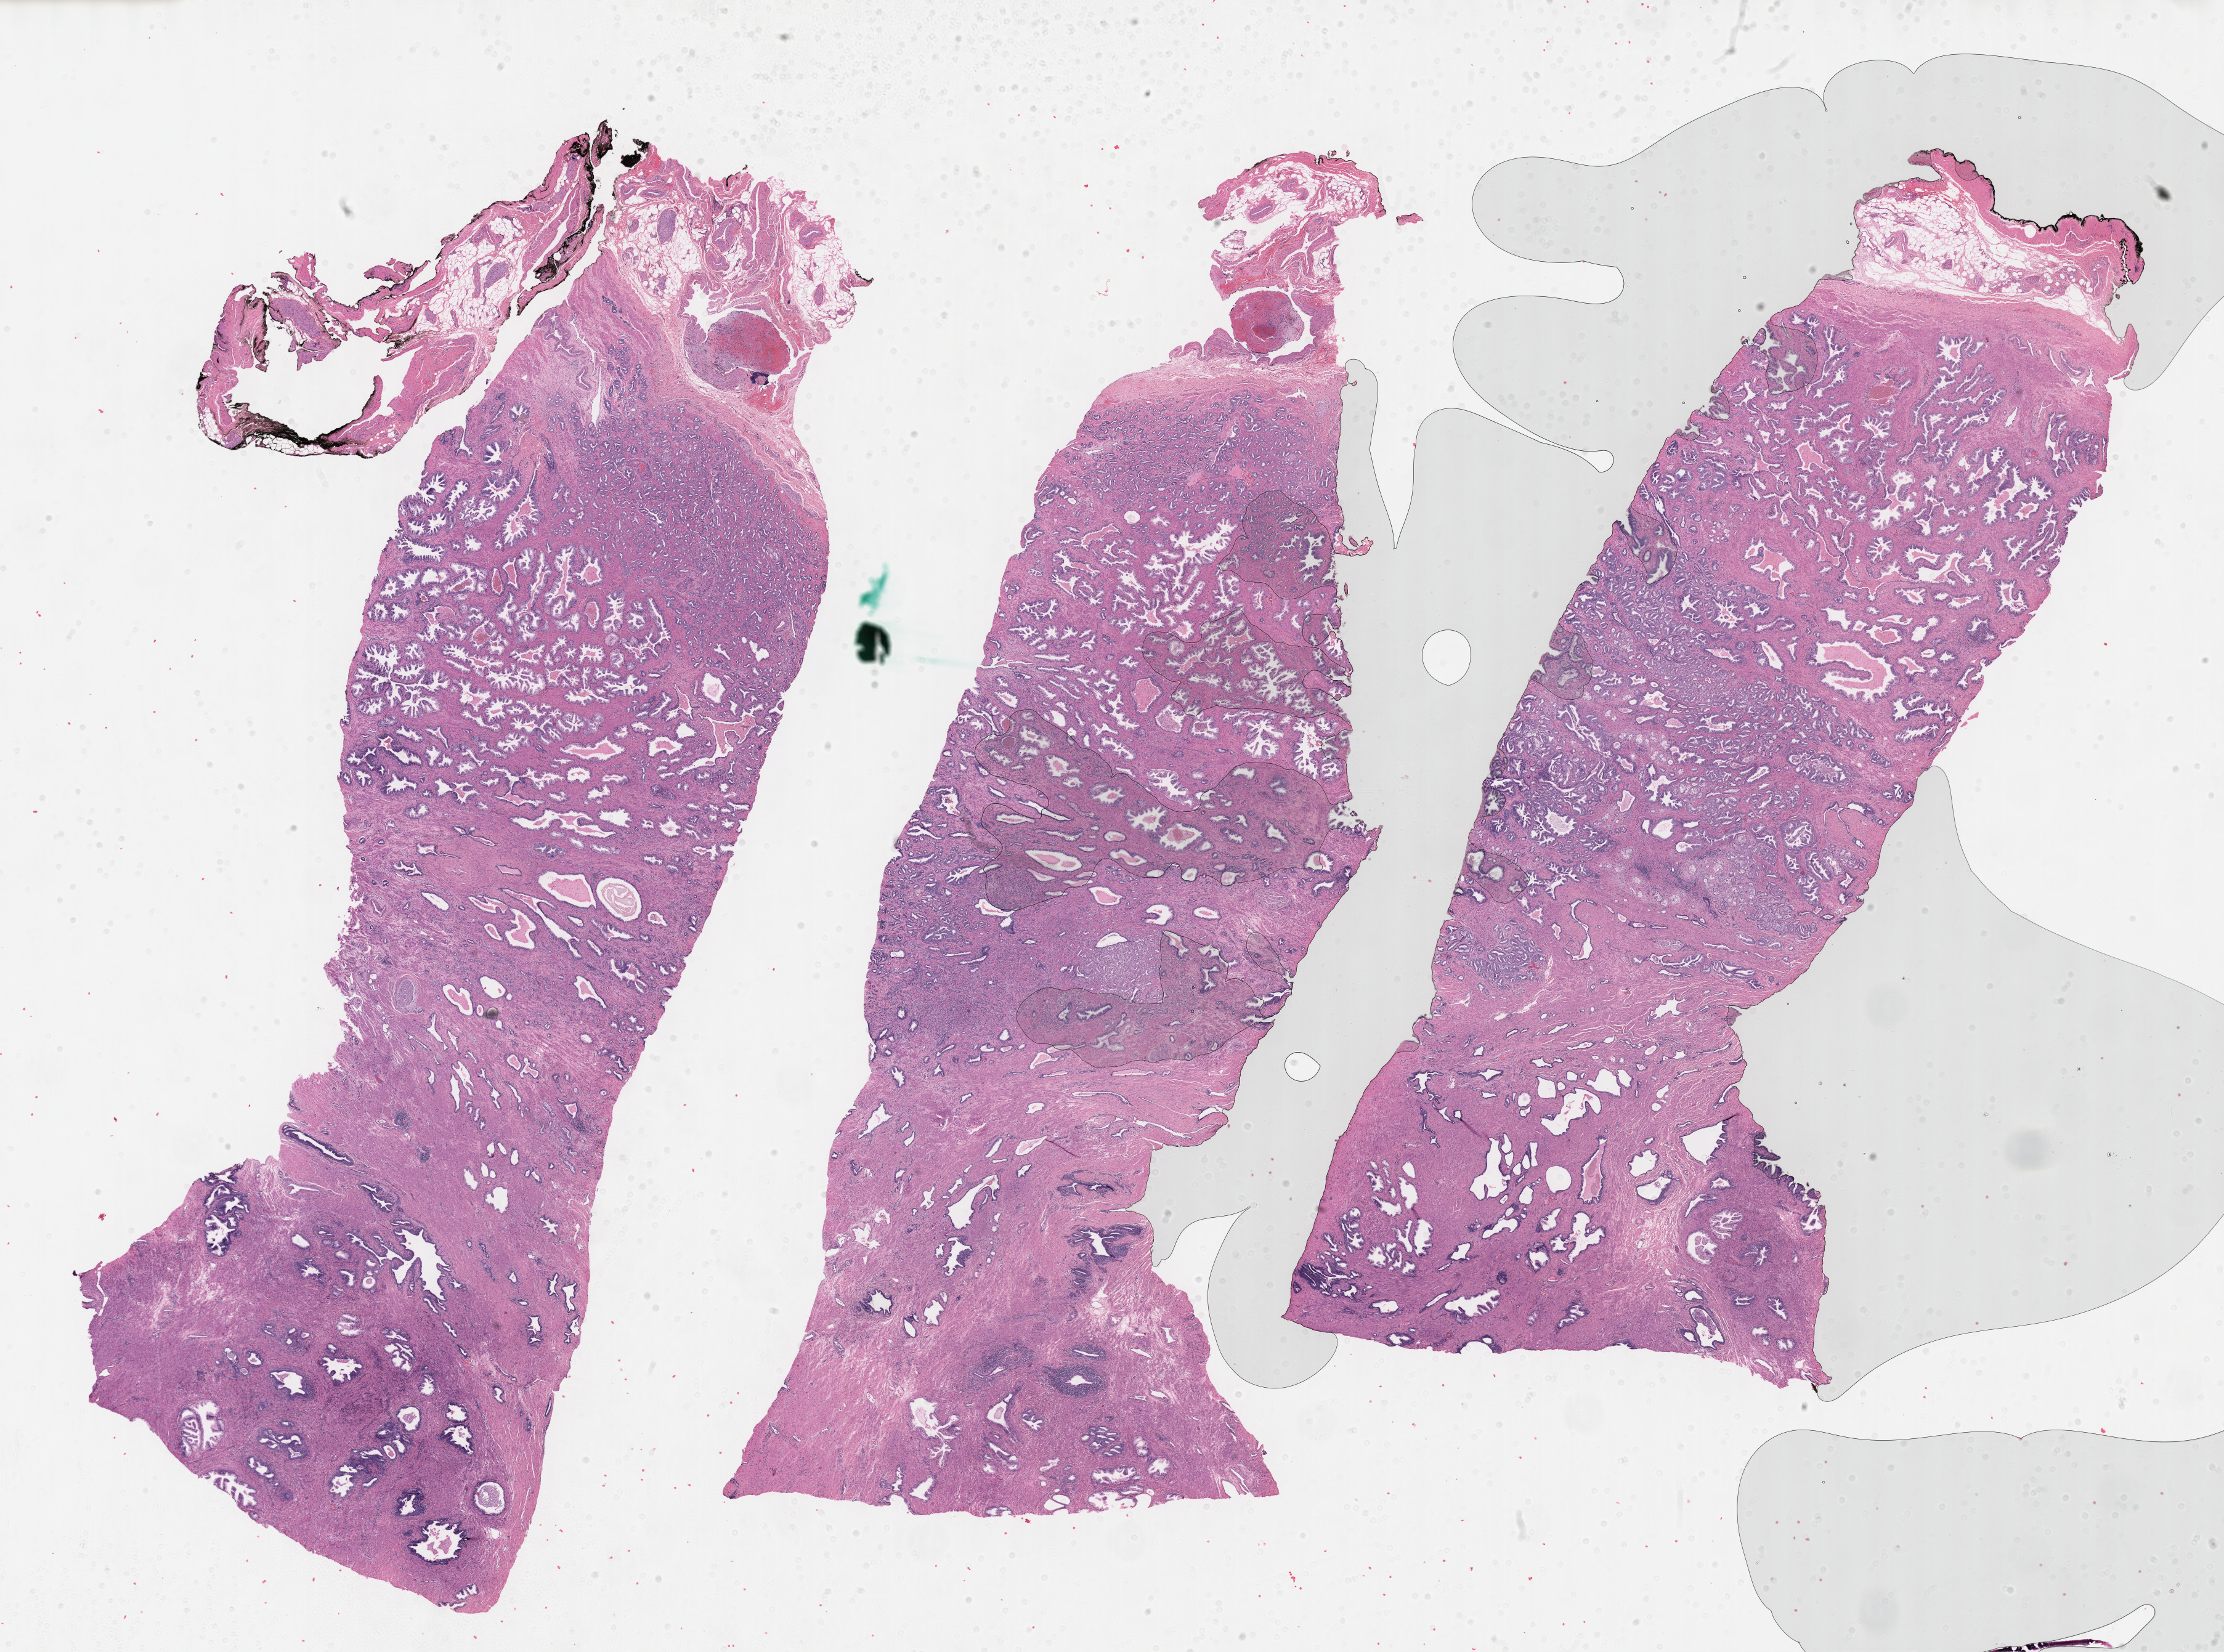
Whole-slide histology image, H&E, a low-resolution overview of the entire scanned area, about 29.2 x 21.7 mm (from a 40x scan). Formalin-fixed paraffin-embedded (FFPE) diagnostic section. Primary tumour sample from the prostate. Male, age 61 years at initial diagnosis. Gleason score: 7 (3+4).
• laterality: bilateral
• histologic diagnosis: Adenocarcinoma, NOS (prostate gland)
• lymph nodes positive (case pathology): 0 of 15 examined